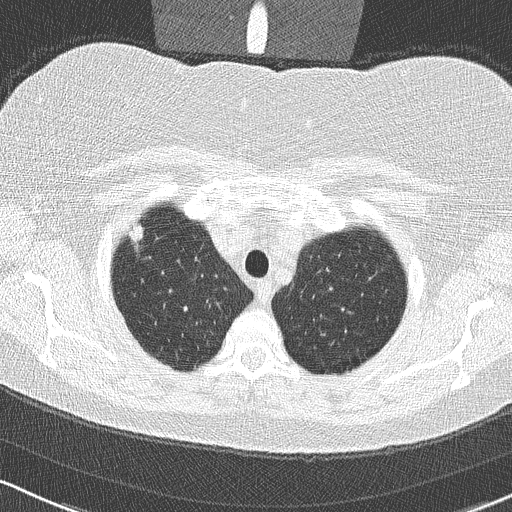
Low-dose screening chest CT, one axial slice; position 273 of 315 along the scan axis; reconstruction kernel B50f; lung window (W 1500 / L -600 HU); 2 mm slice thickness; 512 × 512 image matrix, field of view 320 × 320 mm.
Outlined on this slice (outlined manually by an expert reader):
- lesion 1 (tumor, upper lobe of right lung): bounding box (x1, y1, x2, y2) in pixels: (129, 225, 143, 242)